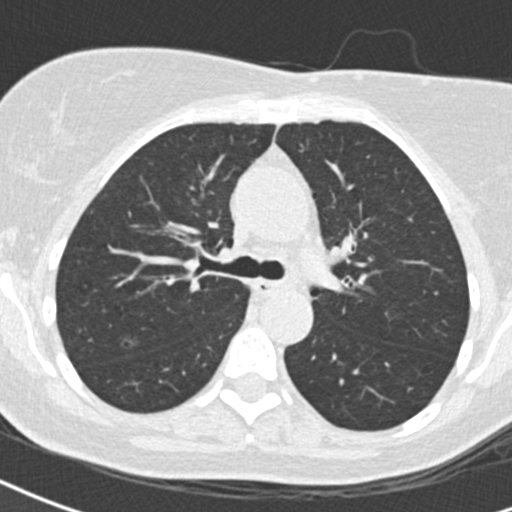
Chest CT (low-dose screening protocol), one axial image, baseline screening round, lung window (W 1500 / L -600 HU), 2 mm slice thickness, standard (soft-tissue) reconstruction kernel (B30f), slice 62 of 184 in the series. Female participant, aged 57 years at enrolment.
- Expert-annotated lung lesion, bounding box [x1, y1, x2, y2] px = [111, 332, 140, 358].
- Reader record for this screening exam (exam-level; its link to the box is not recorded): non-calcified nodule or mass ≥4 mm, left upper lobe, 10 × 9 mm, spiculated (stellate) margins, soft tissue attenuation.
- Note: the box lies in the patient's right hemithorax on this image, whereas the reader's record names the left lung; they may be different findings.
- Participant outcome: lung cancer diagnosed 153 days after this screen — non-small cell carcinoma, right upper lobe, stage IA (AJCC 6th edition), 13 mm at pathology.